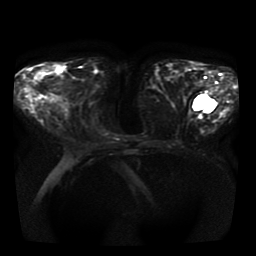
Breast MRI, one axial slice. Position 16 of 41 along the scan axis. Diffusion-weighted series; image 2 of 4 stored at this slice position (different b-values; order by instance number). 1.5 T. 5 mm slice thickness. 256 × 256 image matrix, field of view 350 × 350 mm. Female patient.
Outlined on this slice (expert manual segmentation):
- tumour on diffusion-weighted imaging: bounding box [x1, y1, x2, y2] px = [27, 69, 41, 82]